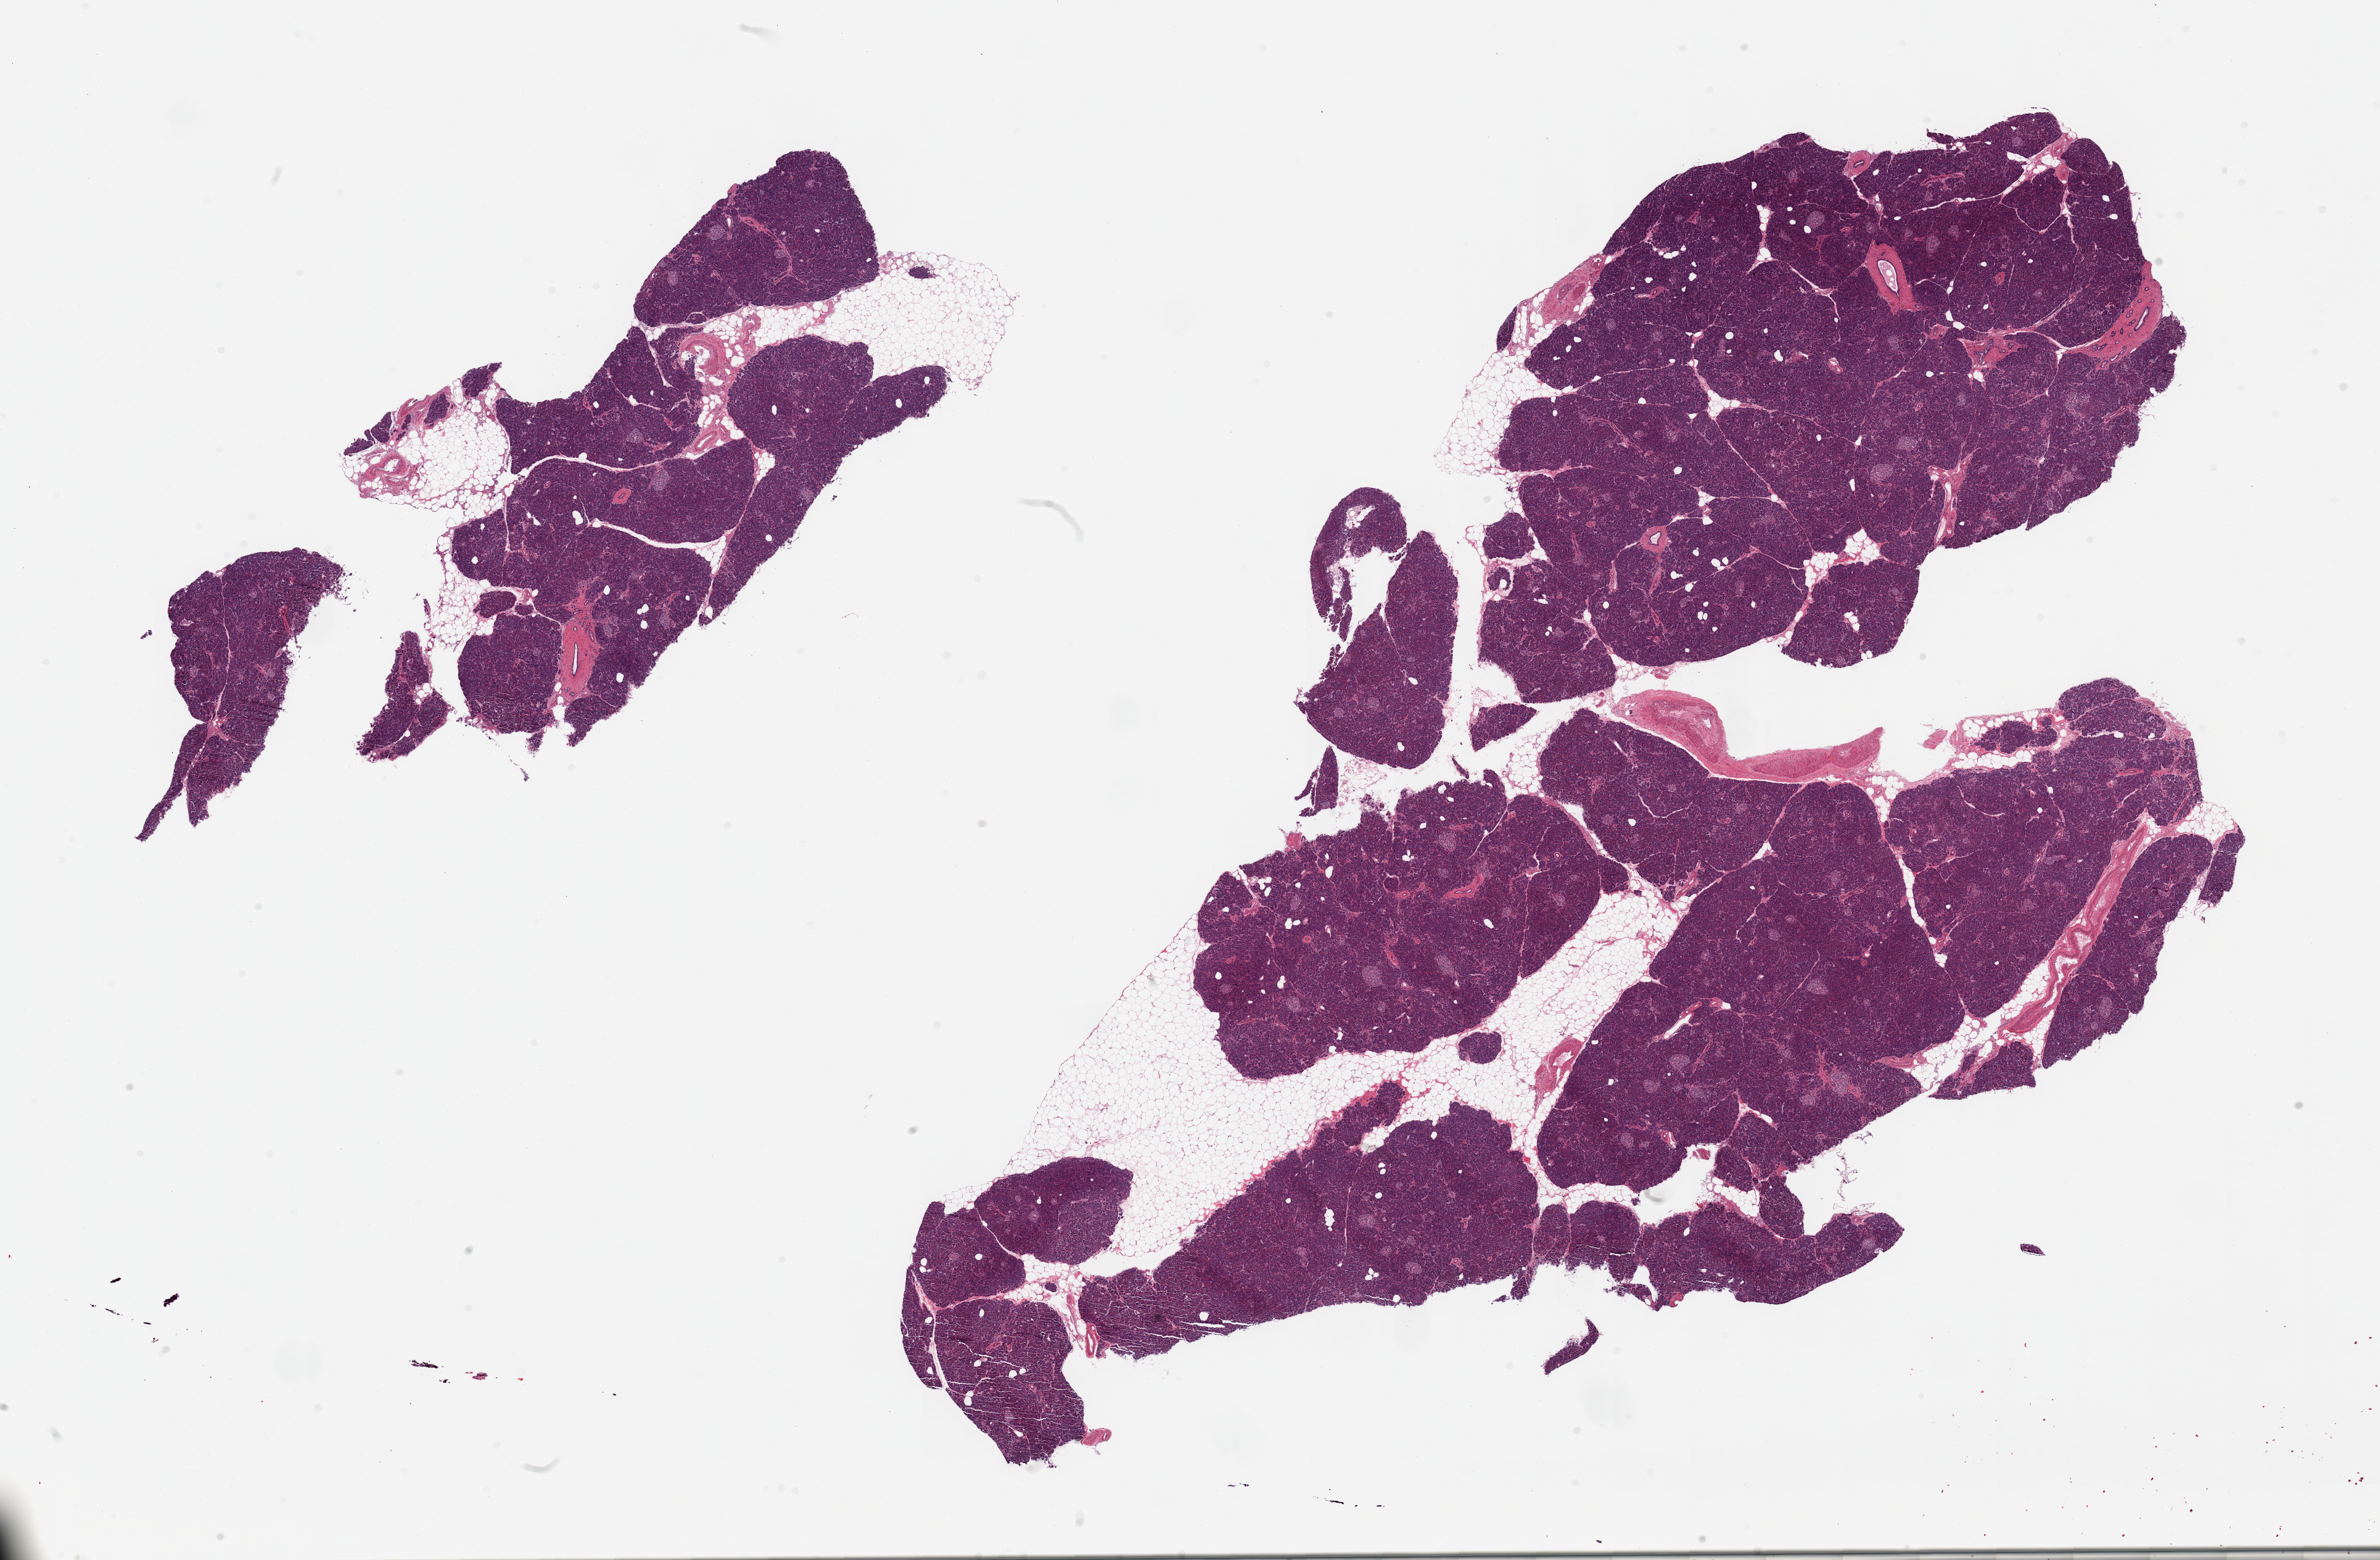
Digitized hematoxylin and eosin (H&E)-stained section, brightfield — a low-resolution overview of the entire scanned area, about 30.5 x 20.0 mm (slide scanned at 20x); PAXgene-fixed paraffin-embedded (PFPE) section; section of pancreas (target tissue); donor tissue sample. Female donor.
Review note (as recorded): 2 pieces, well preserved, numerous Islets, trace fat, excellent specimen.